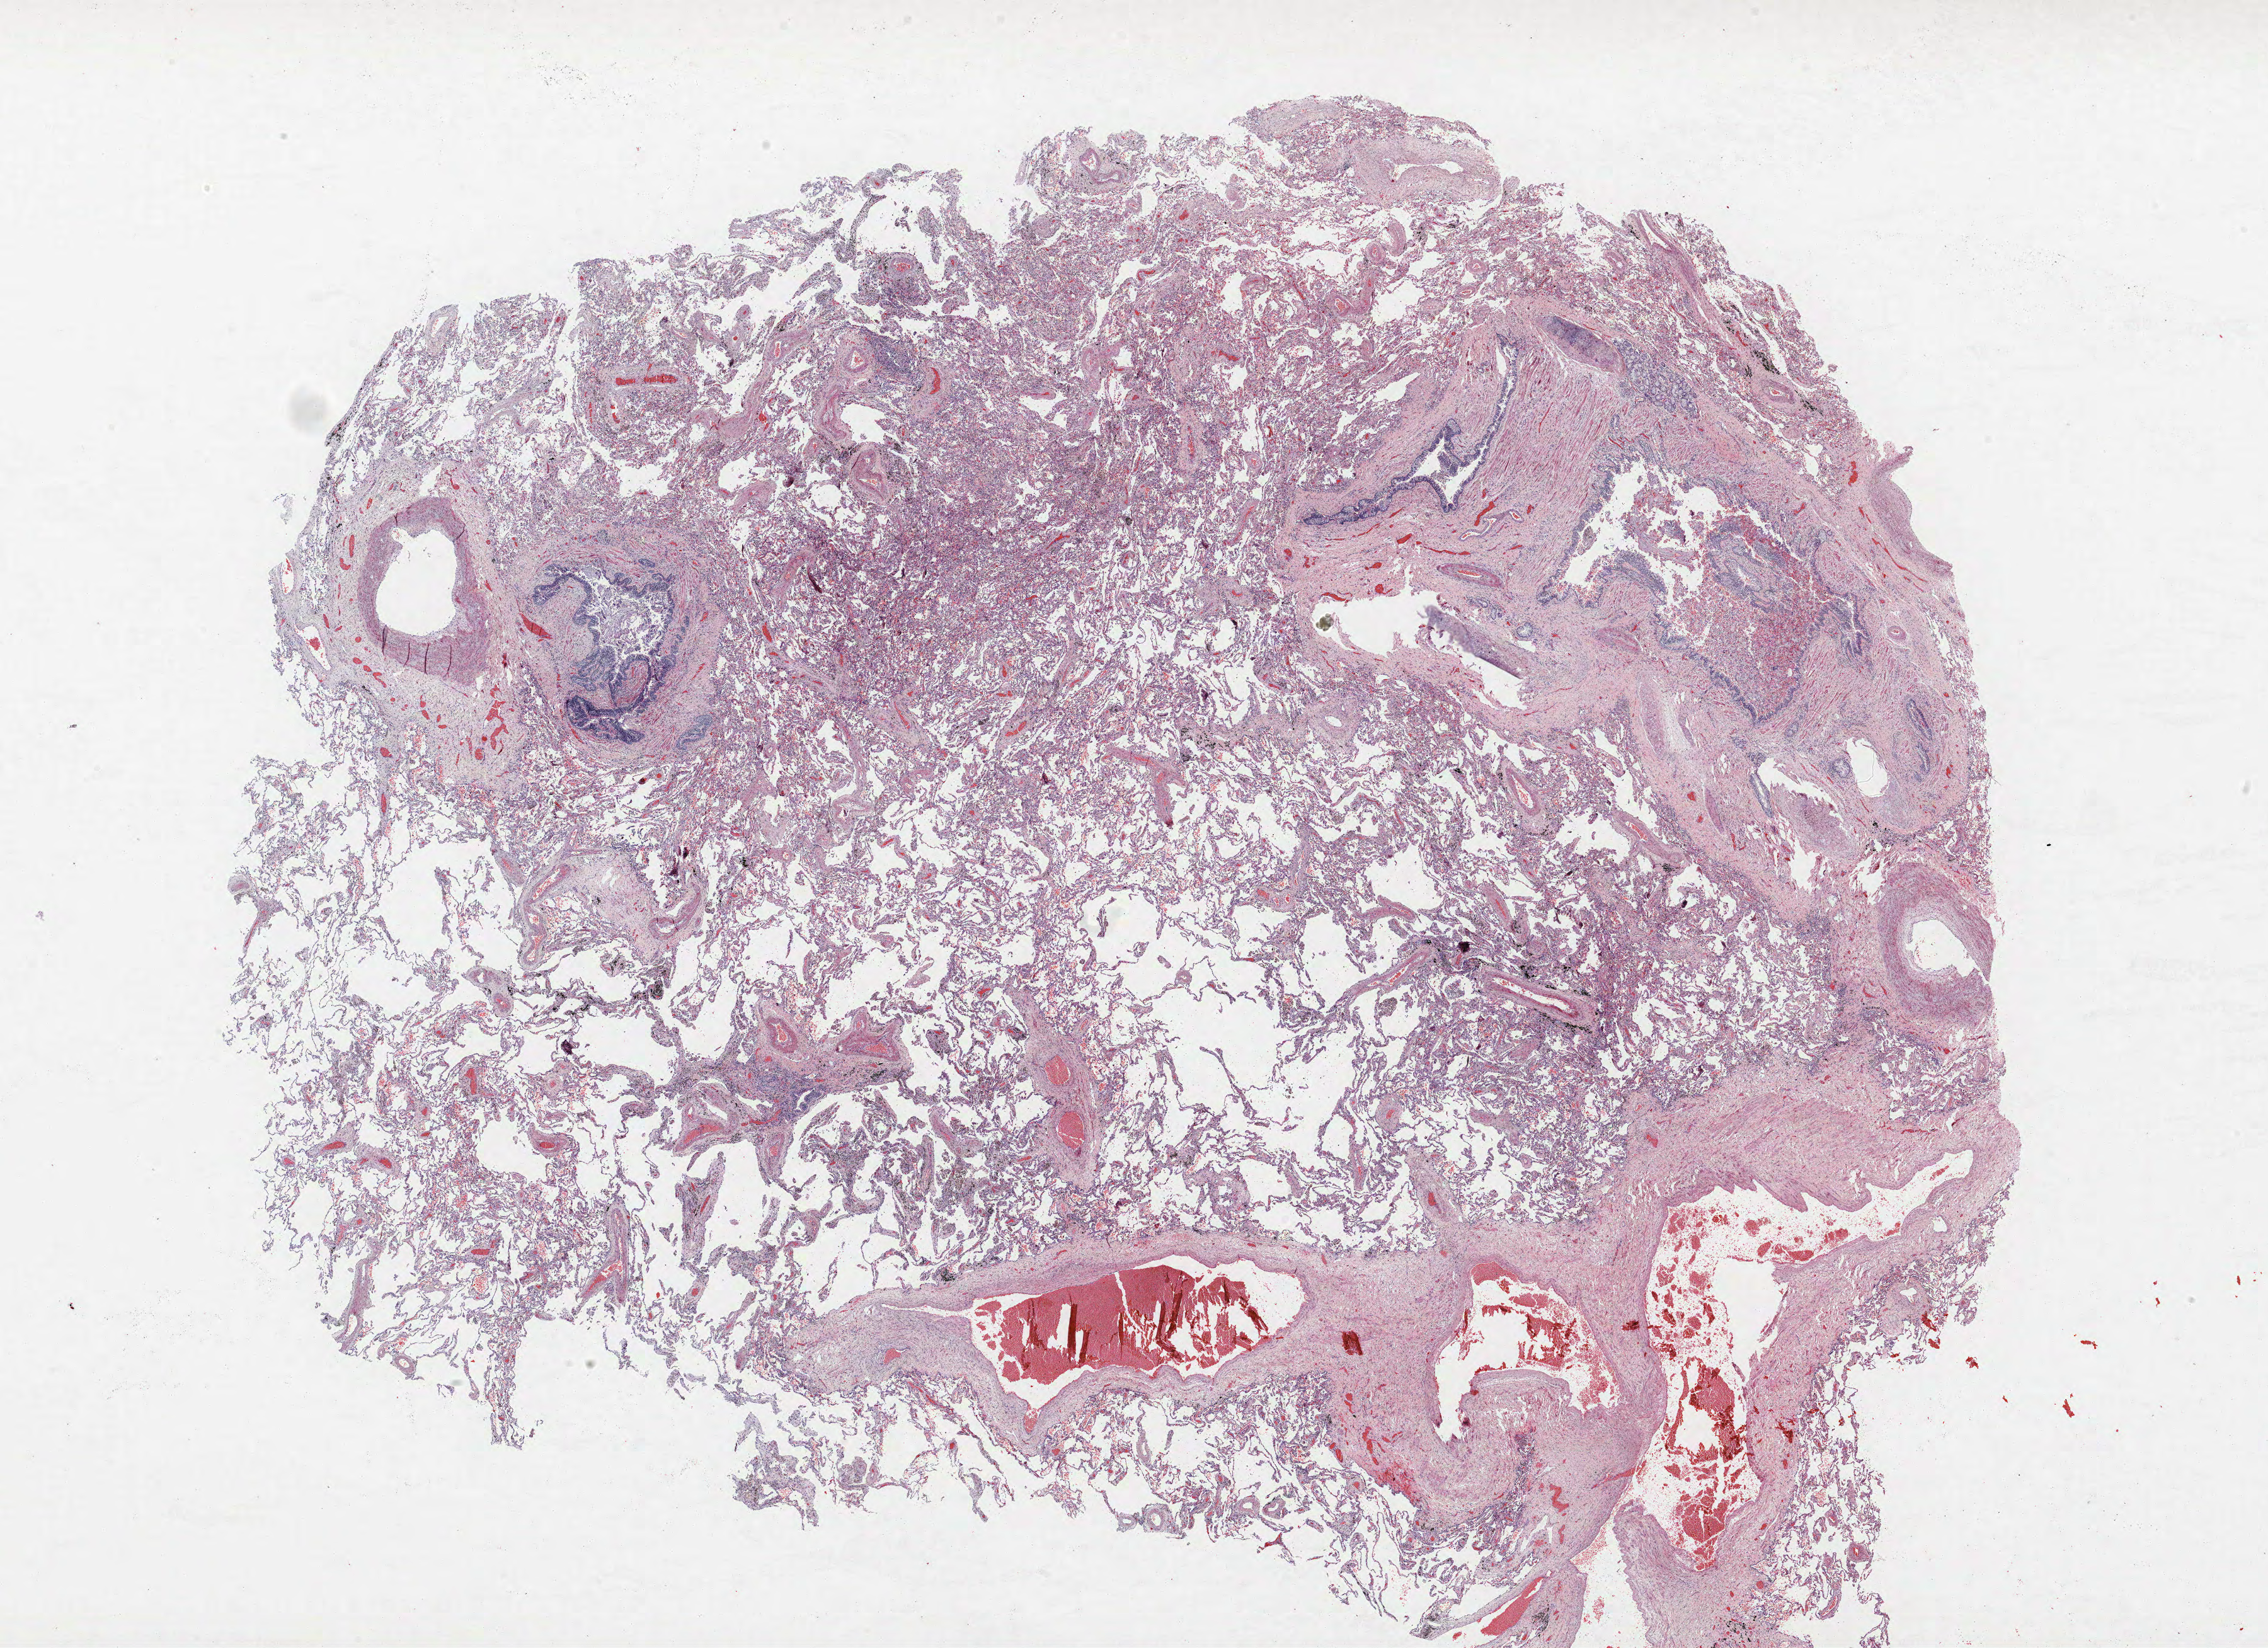
Whole-slide histology image, H&E, low-resolution overview of the scanned area, about 28.8 x 20.9 mm, FFPE section, lung tissue. Male, age 62 at enrolment. Grade: cannot be assessed (GX).
• ICD-O-3 topography: main bronchus (C34.0)
• participant's lung-cancer diagnosis: Squamous cell carcinoma, NOS
• primary tumour location (clinical record): left main stem bronchus
• stage (AJCC 6th edition): IB
• tumour size (pathology): 35 mm